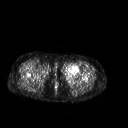
FDG PET of an extremity soft-tissue mass (from a PET/CT study), one axial slice. Slice 253 of 267 in the series (ordered by position). 3.27 mm slice thickness. 128 × 128 image matrix, field of view 500 × 500 mm. Female patient, age 42 years. From the clinical record (not read from this slice): histological type: pleiomorphic leiomyosarcoma; grade: intermediate; site of the primary tumour: left thigh.
Annotated regions visible in this slice (expert contour drawn on MRI and transferred to this co-registered scan by the dataset authors):
- gross tumour volume including surrounding oedema: bounding box (x1, y1, x2, y2) in pixels: (62, 63, 80, 78)
- gross tumour volume (mass): (62, 63, 80, 78)